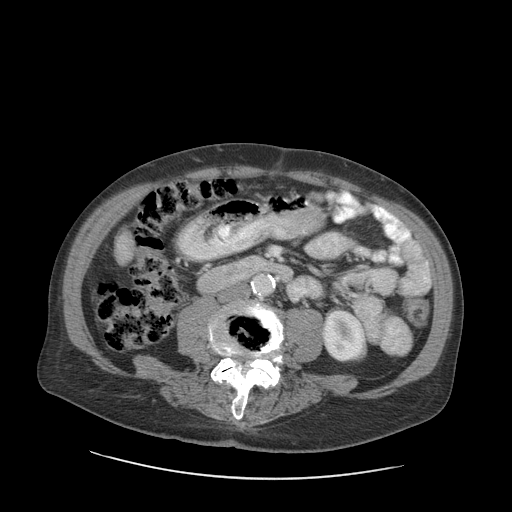
Contrast-enhanced abdominal CT (liver protocol), one axial slice; position 17 of 89 along the scan axis; 140 kVp; soft-tissue window (W 400 / L 40 HU); 2.5 mm slice thickness; 512 × 512 image matrix. Case-level facts recorded for this patient, not image findings: diagnosis: hepatocellular carcinoma (patient treated with transarterial chemoembolisation; whether this scan precedes or follows treatment is not stated here); TNM stage (as recorded): Stage-I; Child-Pugh class: A; tumour nodularity: uninodular.
Annotated regions visible in this slice (semi-automatically segmented with operator editing):
- liver parenchyma outside the tumour (the mass and vessels are separate outlines, so this box may not span the whole liver): bounding box <114,232,132,264> (left, top, right, bottom; pixels)